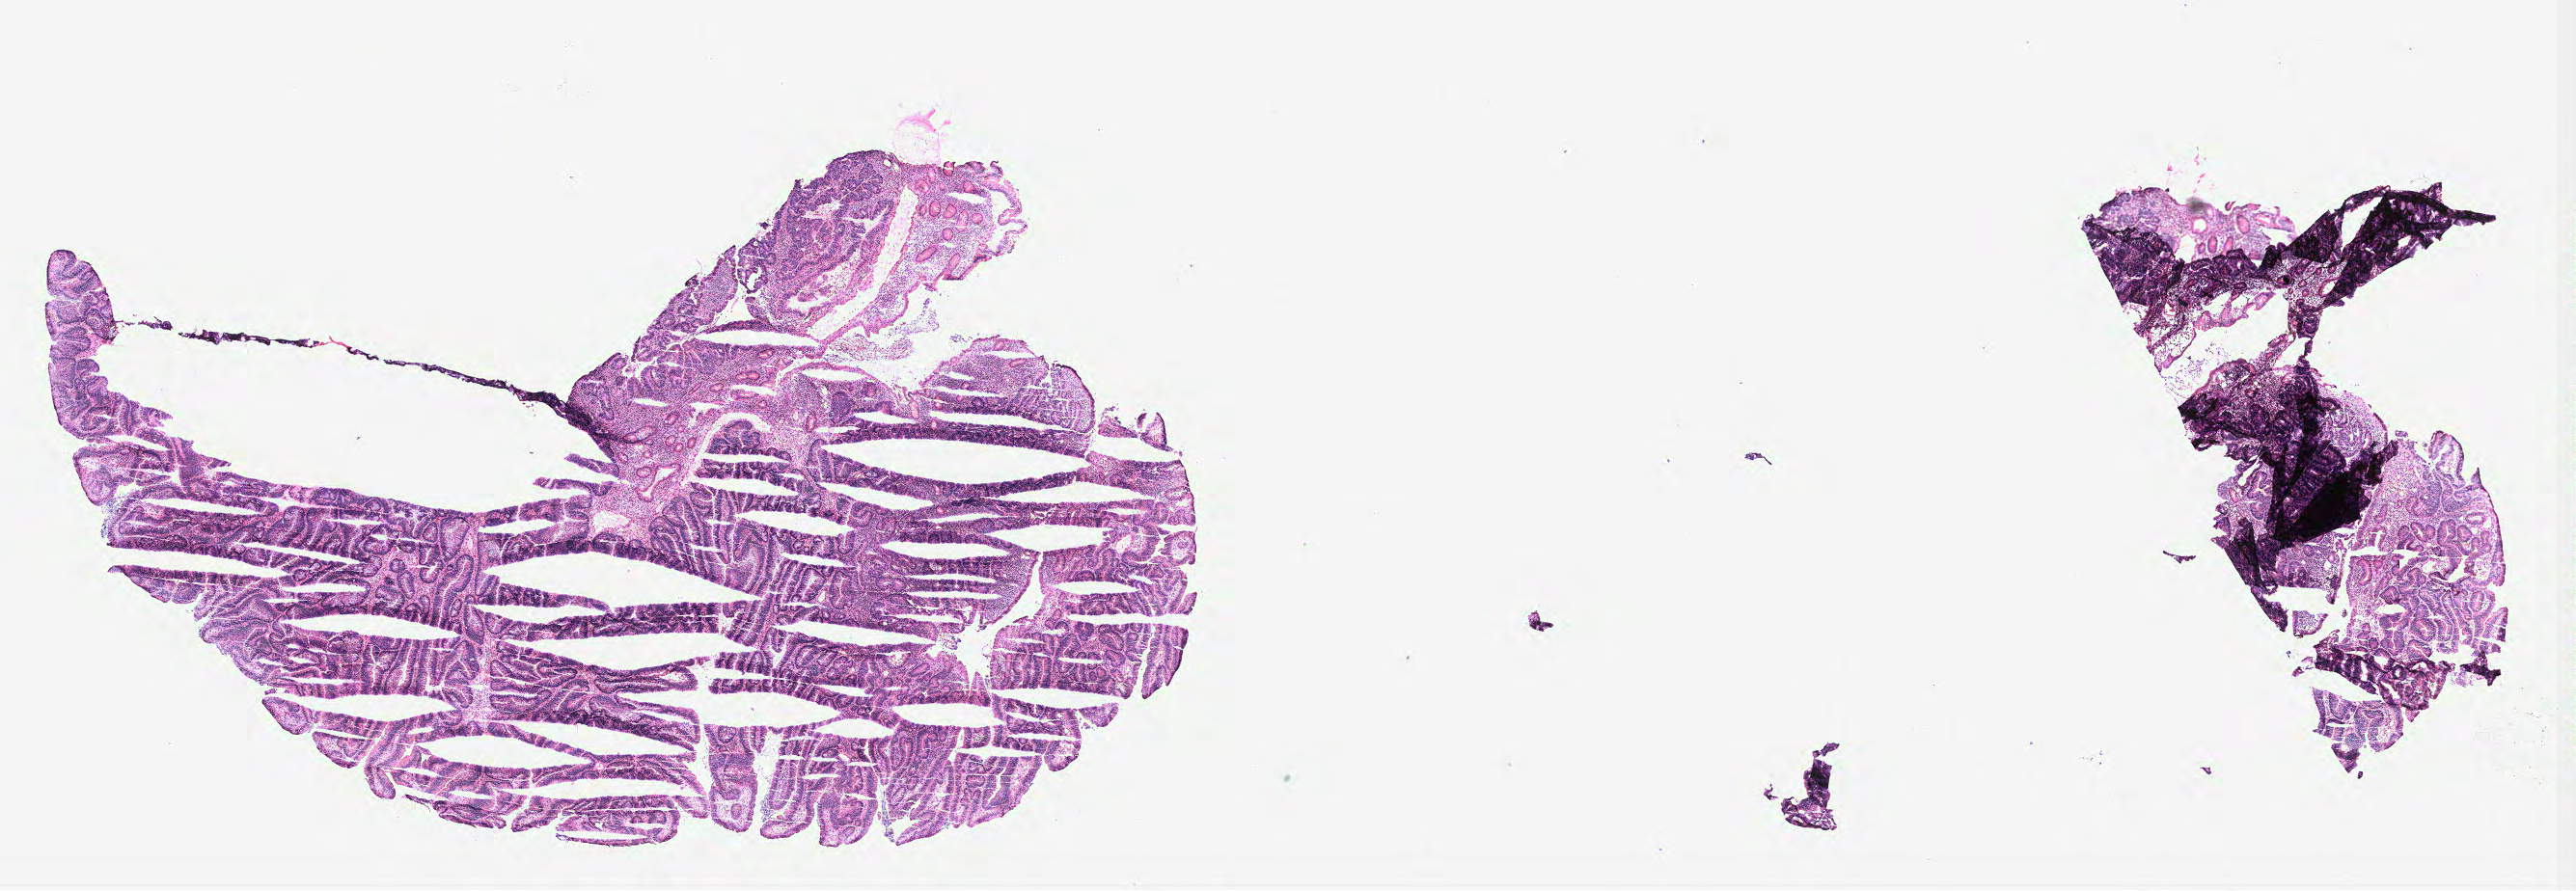
H&E whole-slide image, shown as a low-resolution overview of the whole scanned area (about 21.4 x 7.4 mm, acquisition: 40x scan), colon, normal (non-tumour) tissue. Patient: male, age 86 years.
This section: normal (non-tumour) tissue from the same patient. Patient diagnosis: Adenocarcinoma, NOS.